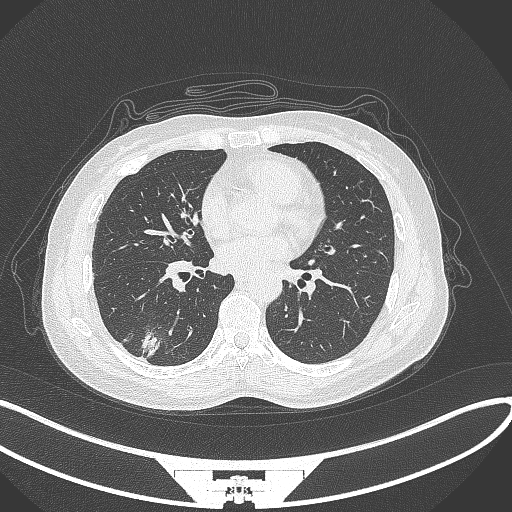
Chest CT, one axial slice; position 134 of 352 along the scan axis; reconstruction kernel B70f; 120 kVp; lung window (W 1500 / L -600 HU); 512 × 512 image matrix, field of view 400 × 400 mm. Patient: female, 55 years. Case-level facts recorded for this patient, not image findings: clinical TNM (as recorded): T1c N1 M0.
Outlined on this slice (bounding box drawn by a radiologist):
- lung tumour (recorded histology: adenocarcinoma): box from (x=140, y=327) to (x=167, y=364) px